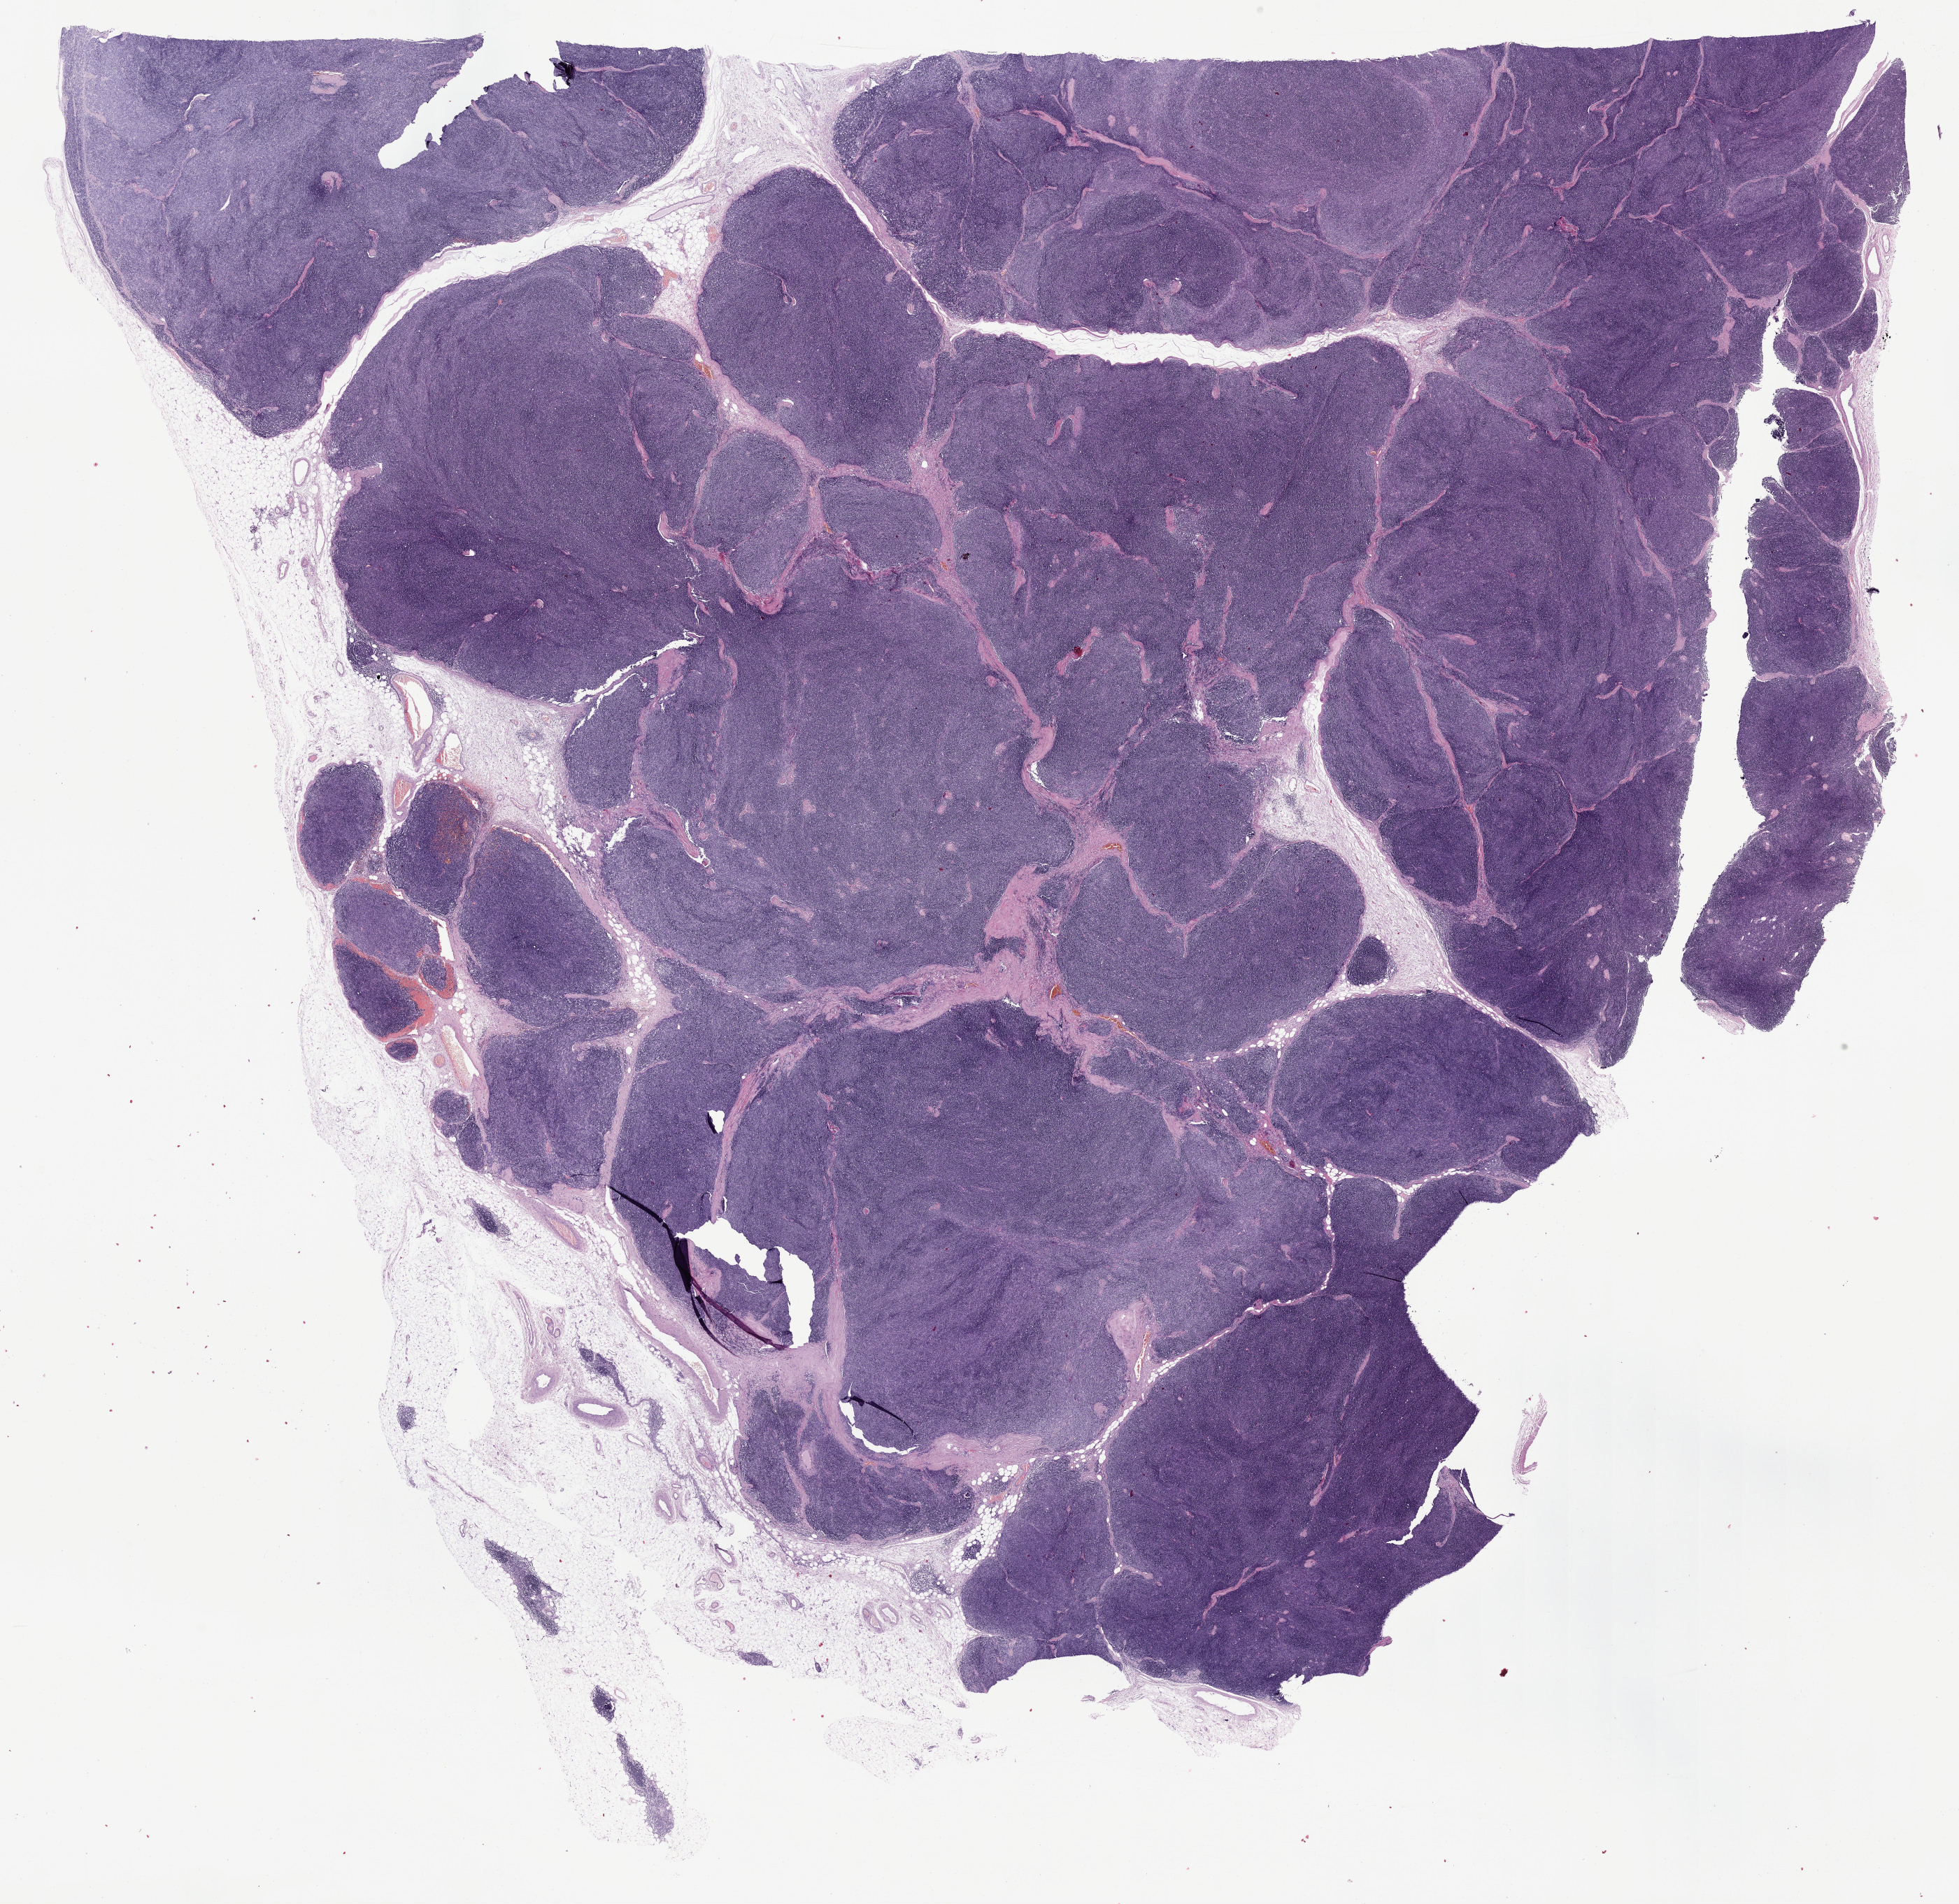
Digitized H&E-stained tissue section (whole slide), low-resolution overview of the scanned area, about 22.7 x 22.0 mm (from a 40x scan). Formalin-fixed paraffin-embedded (FFPE) diagnostic section. Sample: primary tumour, thymus. Patient: female, age at initial diagnosis 74 years.
* histologic diagnosis: Thymoma, type AB, malignant